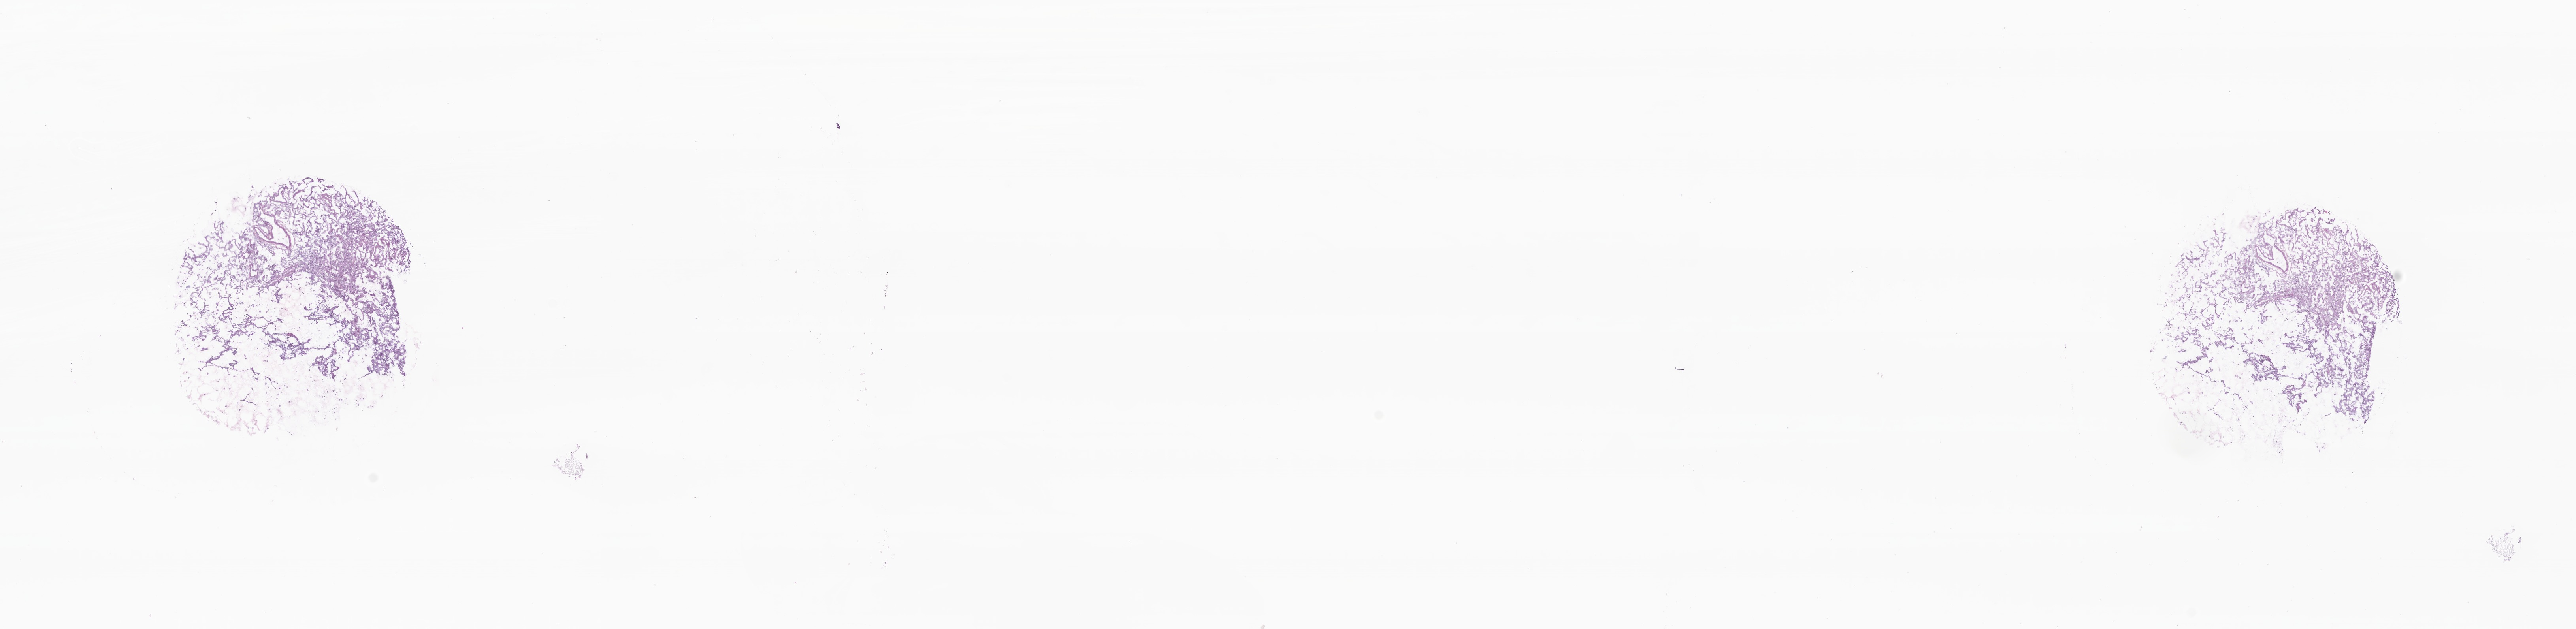
Hematoxylin and eosin (H&E) whole-slide image, whole scanned area (about 27.5 x 6.7 mm) shown as a low-resolution overview. Cryosection. Specimen: primary tumor. Site: upper lobe of left lung. Female patient; age at initial diagnosis 52 years. Composition of this section per pathologist review: tumor cells 100%, tumor nuclei 0%, stromal cells 0%, necrosis 0%, normal cells 0%. Inflammatory infiltration, as recorded: lymphocyte infiltration 0%, monocyte infiltration 0%, neutrophil infiltration 0%.
- section: bottom of the tissue portion
- histologic diagnosis: Adenocarcinoma of lung, mucinous